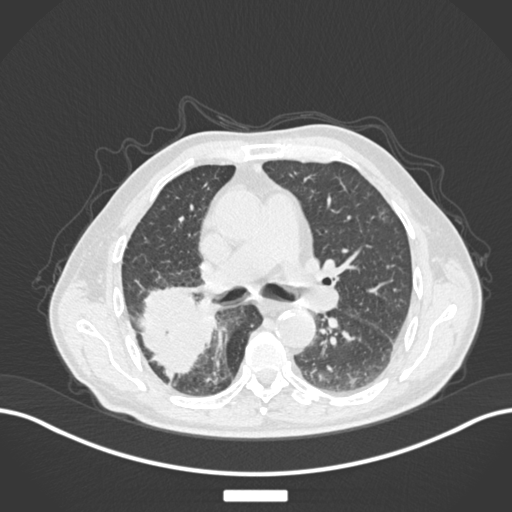
Chest CT, one axial slice. Slice 102 of 201 in the series (ordered by position). 120 kVp. Lung window (W 1500 / L -600 HU). 512 × 512 image matrix, field of view 400 × 400 mm. Male patient, age 72 years. From the clinical record (not read from this slice): clinical TNM (as recorded): T3 N2 M0.
Outlined on this slice (bounding box drawn by a radiologist):
- lung tumour (recorded histology: adenocarcinoma): bounding box [x1, y1, x2, y2] px = [137, 284, 213, 380]